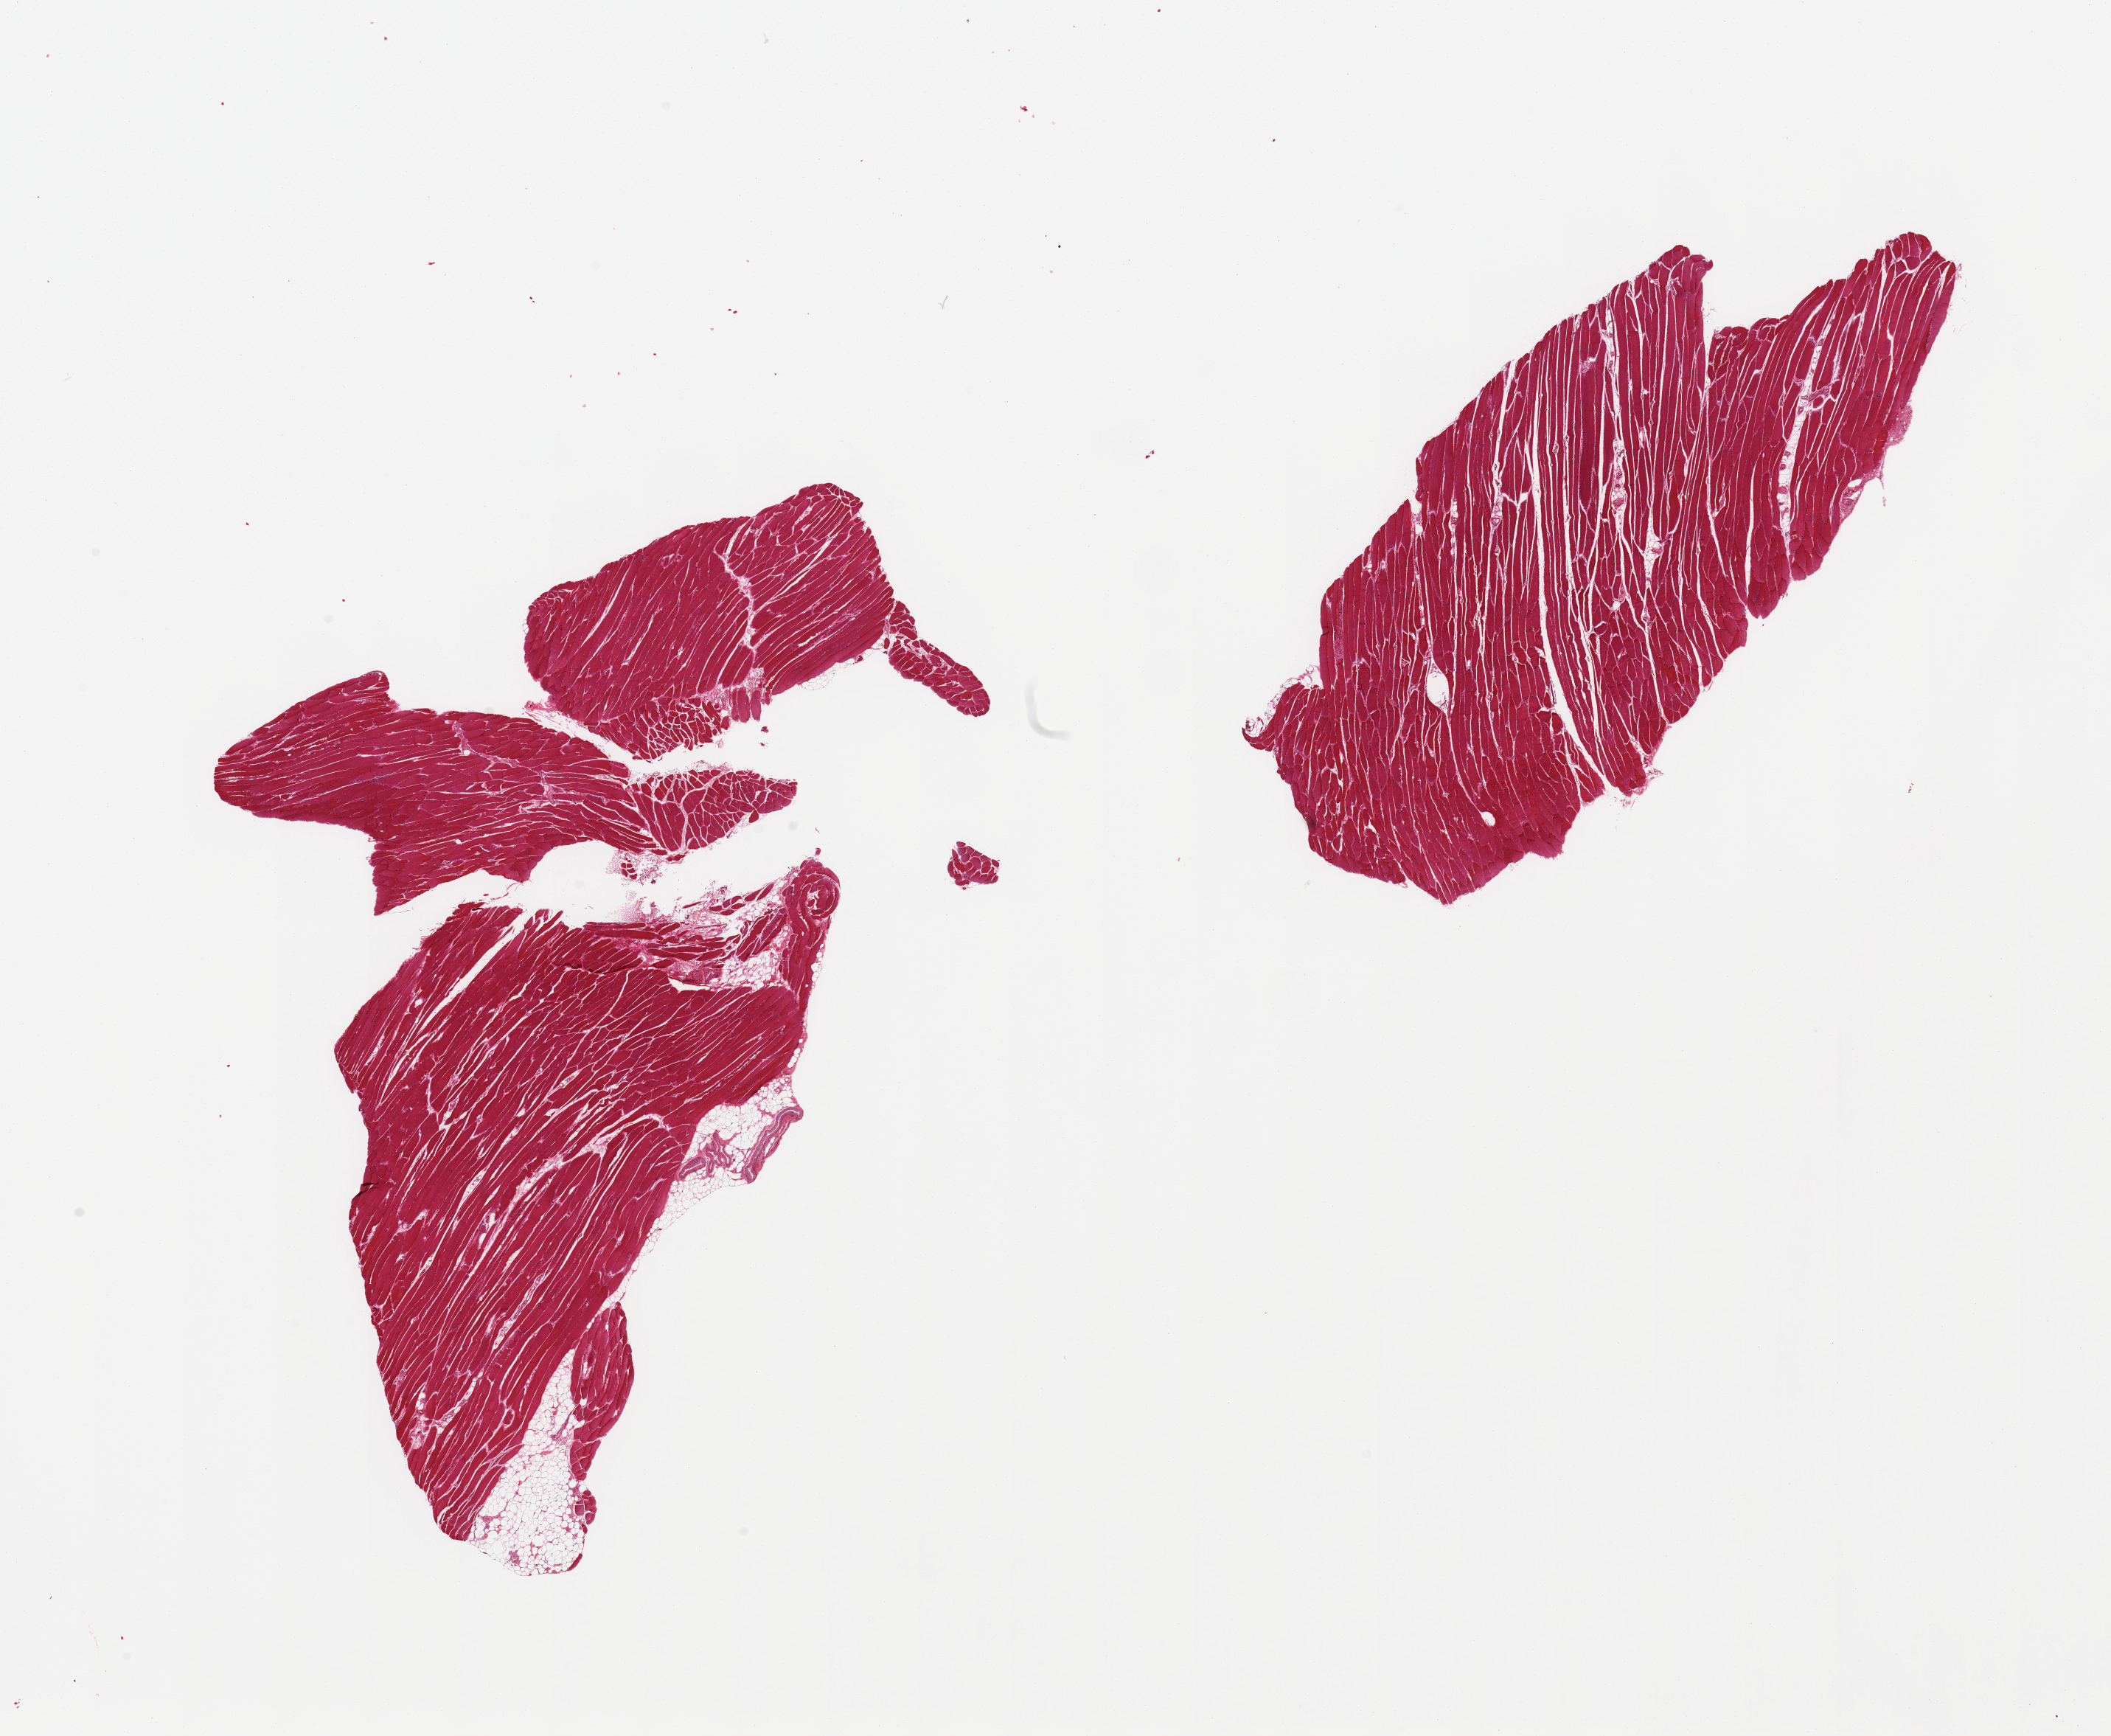
Digitized H&E-stained section, a low-resolution overview of the entire scanned area, about 22.6 x 18.6 mm. PAXgene-fixed paraffin-embedded (PFPE) section. Section of skeletal muscle (target tissue). Tissue donor sample.
Pathologist's review note for this sample: 2 pieces; 1% fat content.